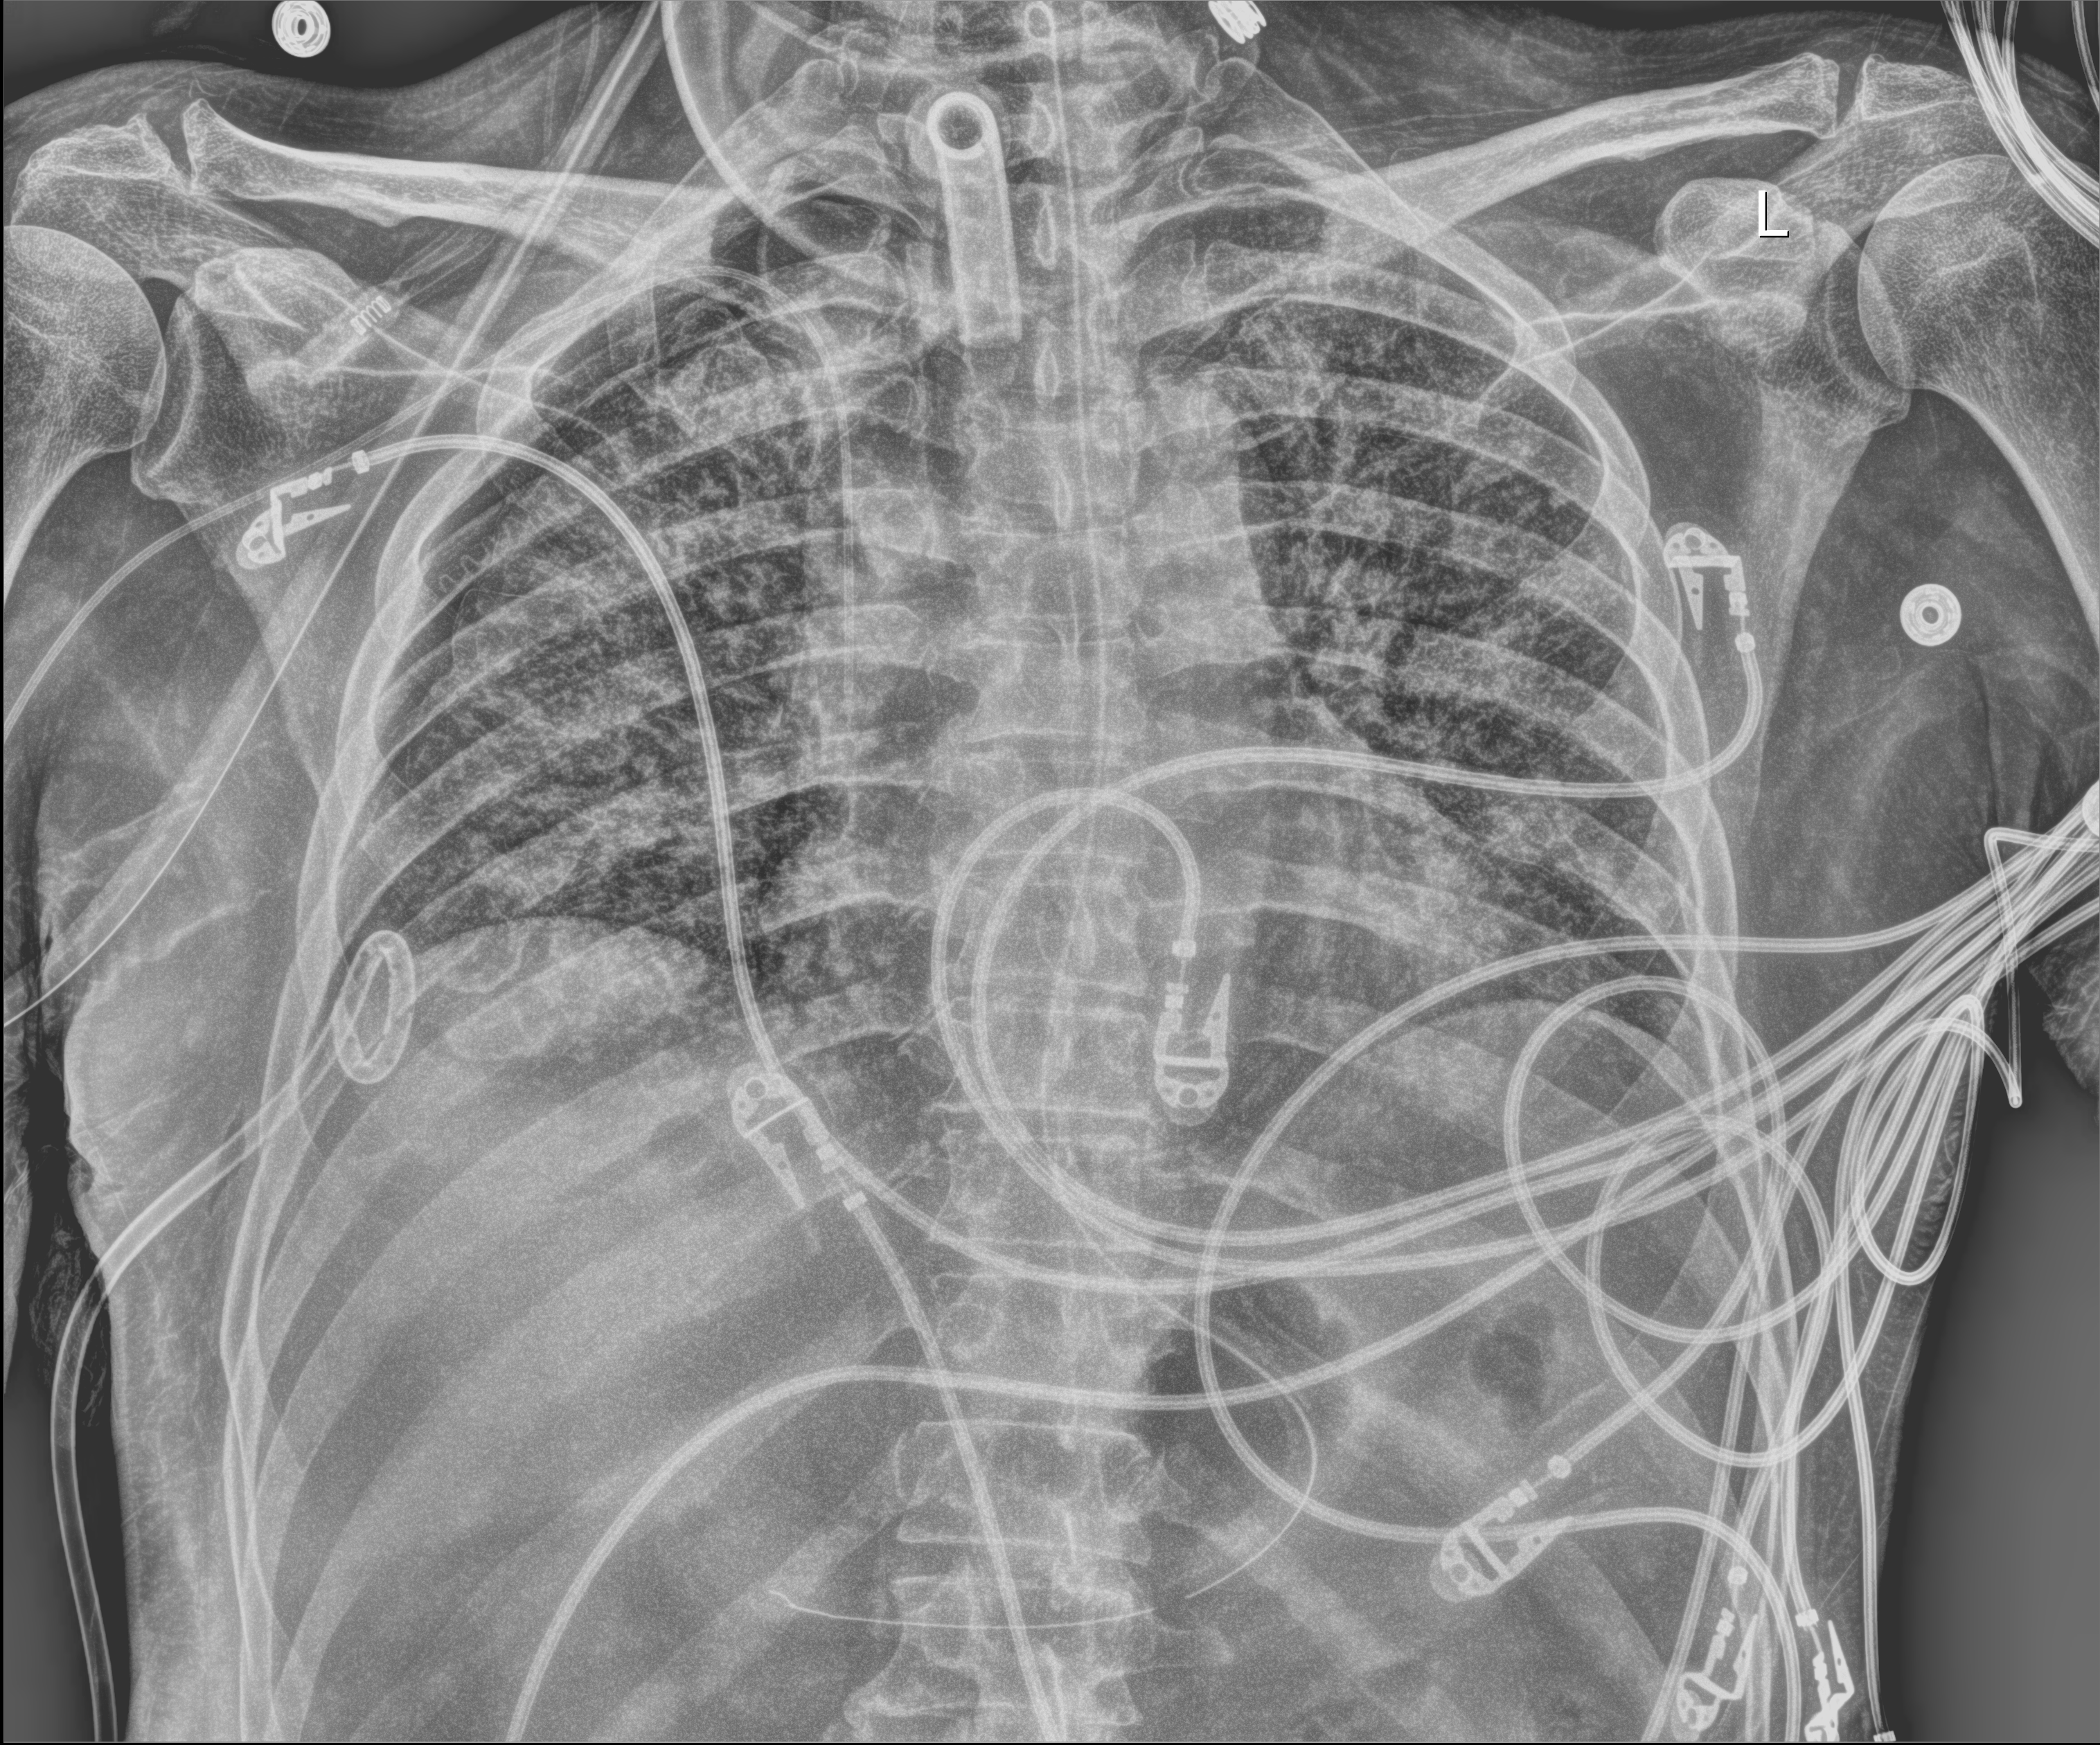
Chest X-ray (portable), anteroposterior (AP) projection. Male patient hospitalised with COVID-19, age 18–59 years.
Admission-level facts for this patient (not findings on this image; timing relative to this image not recorded): admitted to intensive care during this hospital stay: yes; mechanically ventilated during this hospital stay: yes; COPD (admission record): no.